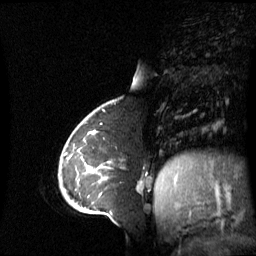
Breast MRI (dynamic contrast-enhanced), one sagittal slice. Position 18 of 60 along the scan axis. Dynamic contrast-enhanced series, image 2 of 3 at this slice position (ordered by acquisition). 1.5 T. TE 4.2 ms, TR 8.4 ms. 256 × 256 image matrix, field of view 270 × 270 mm. Female patient, age 43 years. From the clinical record (not read from this slice): setting: breast cancer imaged before/during neoadjuvant chemotherapy; receptor status: triple-negative.
Structures marked on this image (semi-automatic segmentation, software-assisted and operator-edited):
- analysis volume of interest (the breast-tissue region the enhancement analysis was run in; not a lesion): bounding box <69,137,143,198> (left, top, right, bottom; pixels)
- tumour enhancement mask (voxels above the 70 % enhancement threshold inside the analysis volume of interest): <69,150,105,179>